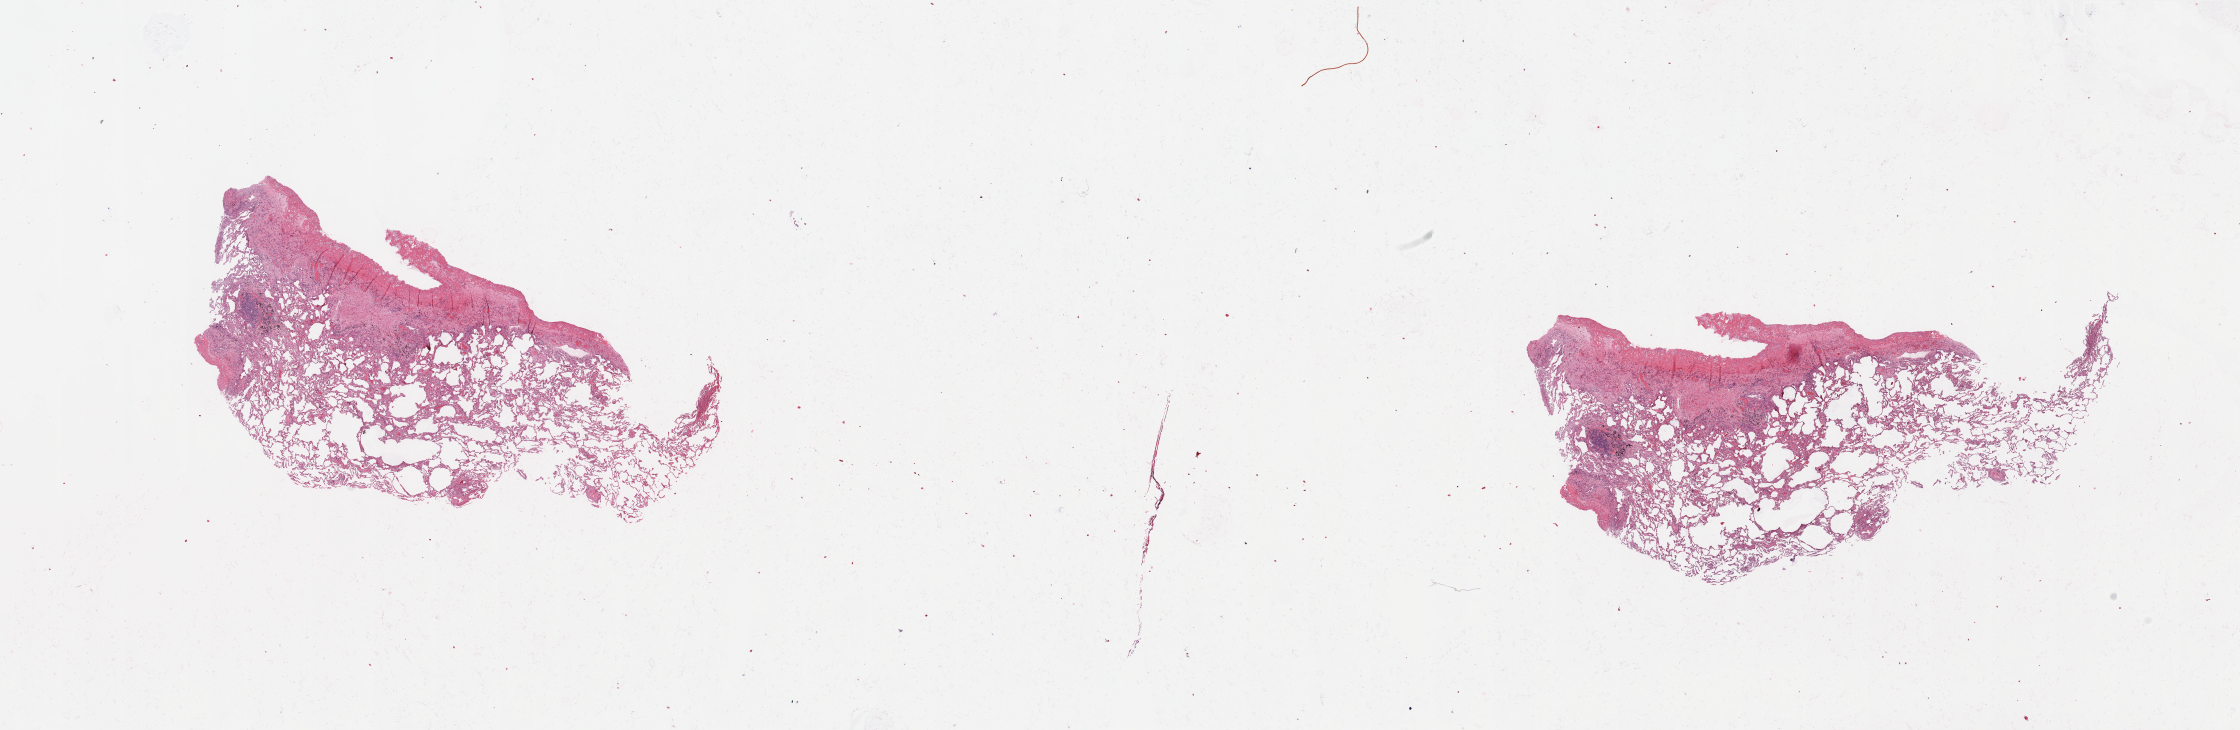
Whole-slide histology image, H&E-stained — whole scanned area (about 35.4 x 11.5 mm, slide scanned at 20x) shown as a low-resolution overview, normal (non-tumour) tissue sample, sampled site: lung. Patient: male, age 57 years.
* this section: normal (non-tumour) tissue from the same patient
* patient diagnosis: Squamous cell carcinoma, NOS